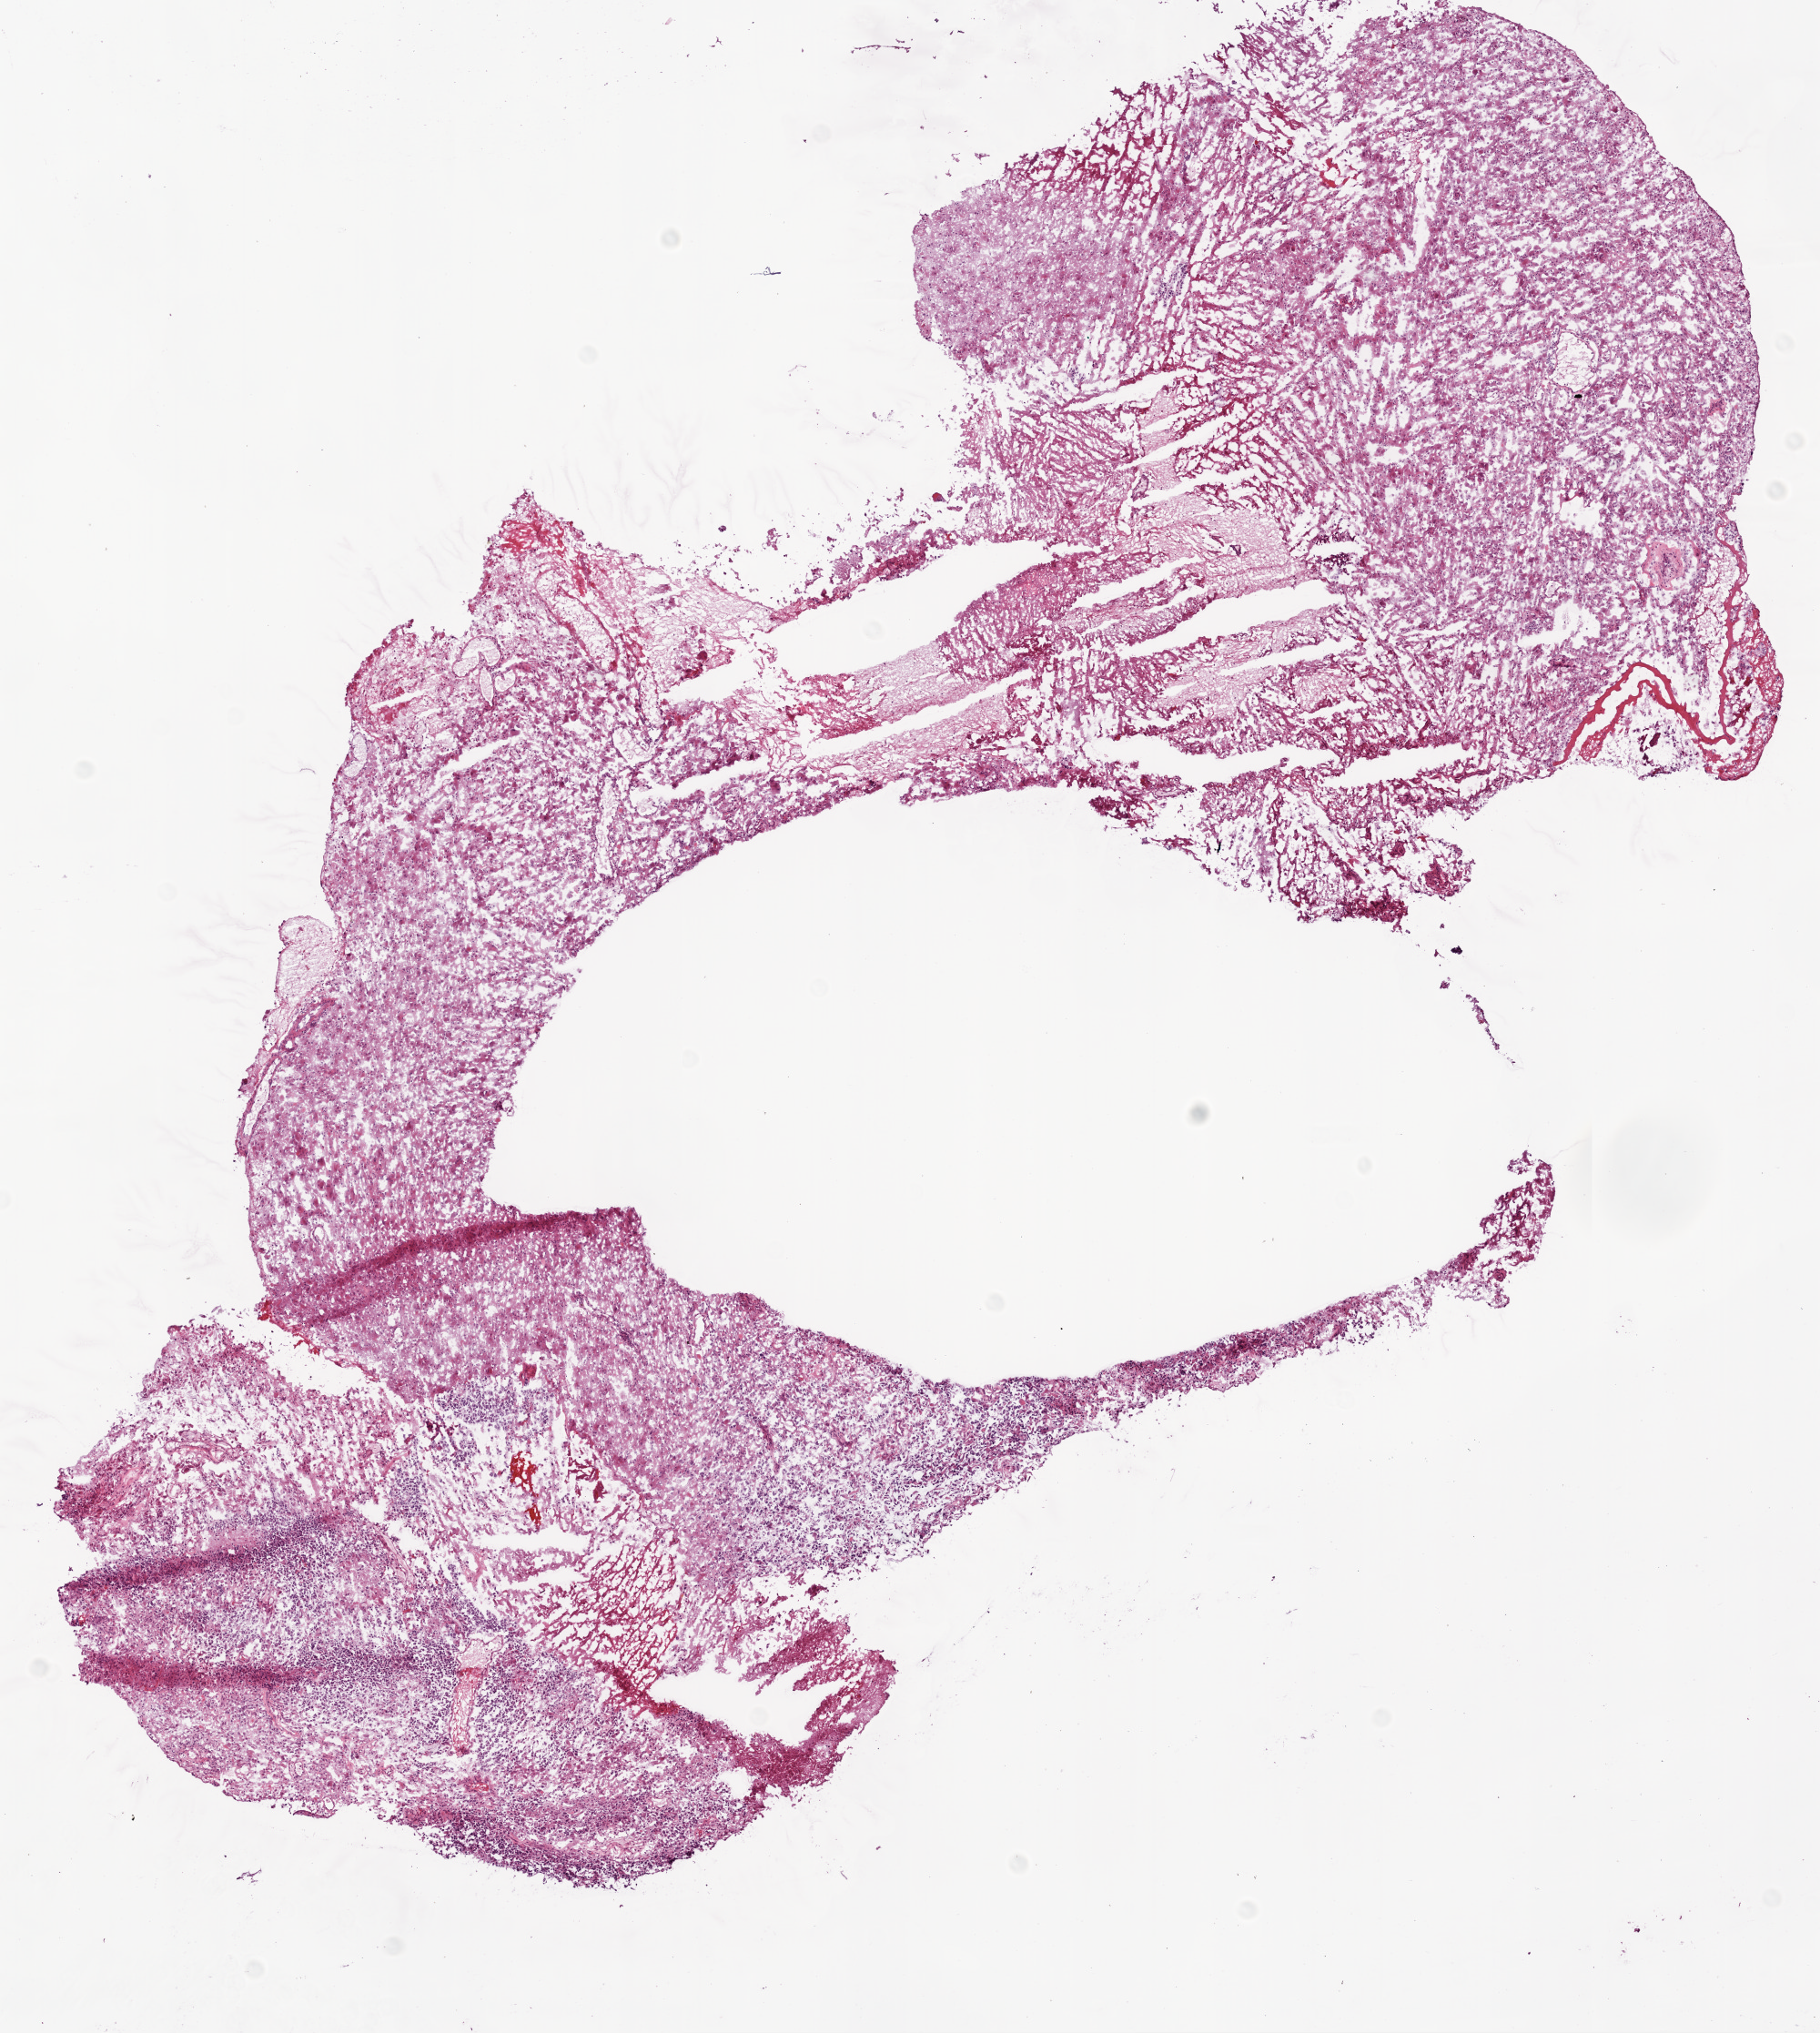
Whole-slide histology image, H&E-stained — a low-resolution overview of the entire scanned area, about 8.0 x 9.0 mm; frozen section from the bottom of the tissue portion; brain, primary tumour sample. Male patient; age at initial diagnosis 58 years. Composition of this section per pathologist review: tumour cells 60%, tumour nuclei 90%, normal cells 0%, stromal cells 10%, necrosis 30%.
Diagnosis: Glioblastoma.